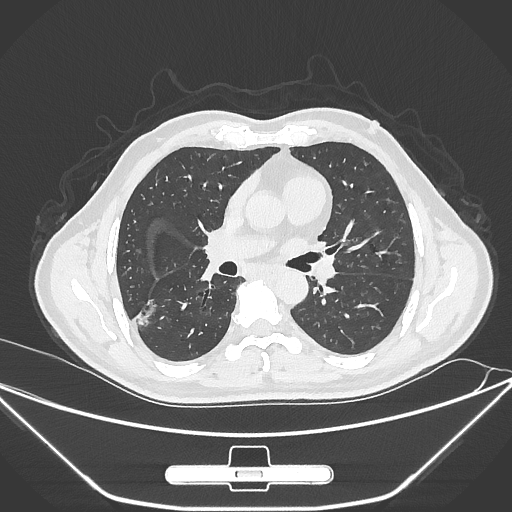
Chest CT, one axial slice. Position 157 of 310 along the scan axis. Reconstruction kernel IMR1,SharpPlus. 120 kVp. Lung window (W 1500 / L -600 HU). 512 × 512 image matrix, field of view 398 × 398 mm. Male patient, age 71 years. Case-level facts recorded for this patient, not image findings: clinical TNM (as recorded): T1c N0 M0; histopathological grade: G2.
Structures marked on this image (bounding box drawn by a radiologist):
- lung tumour (recorded histology: adenocarcinoma): bounding box (x1, y1, x2, y2) in pixels: (134, 294, 157, 331)